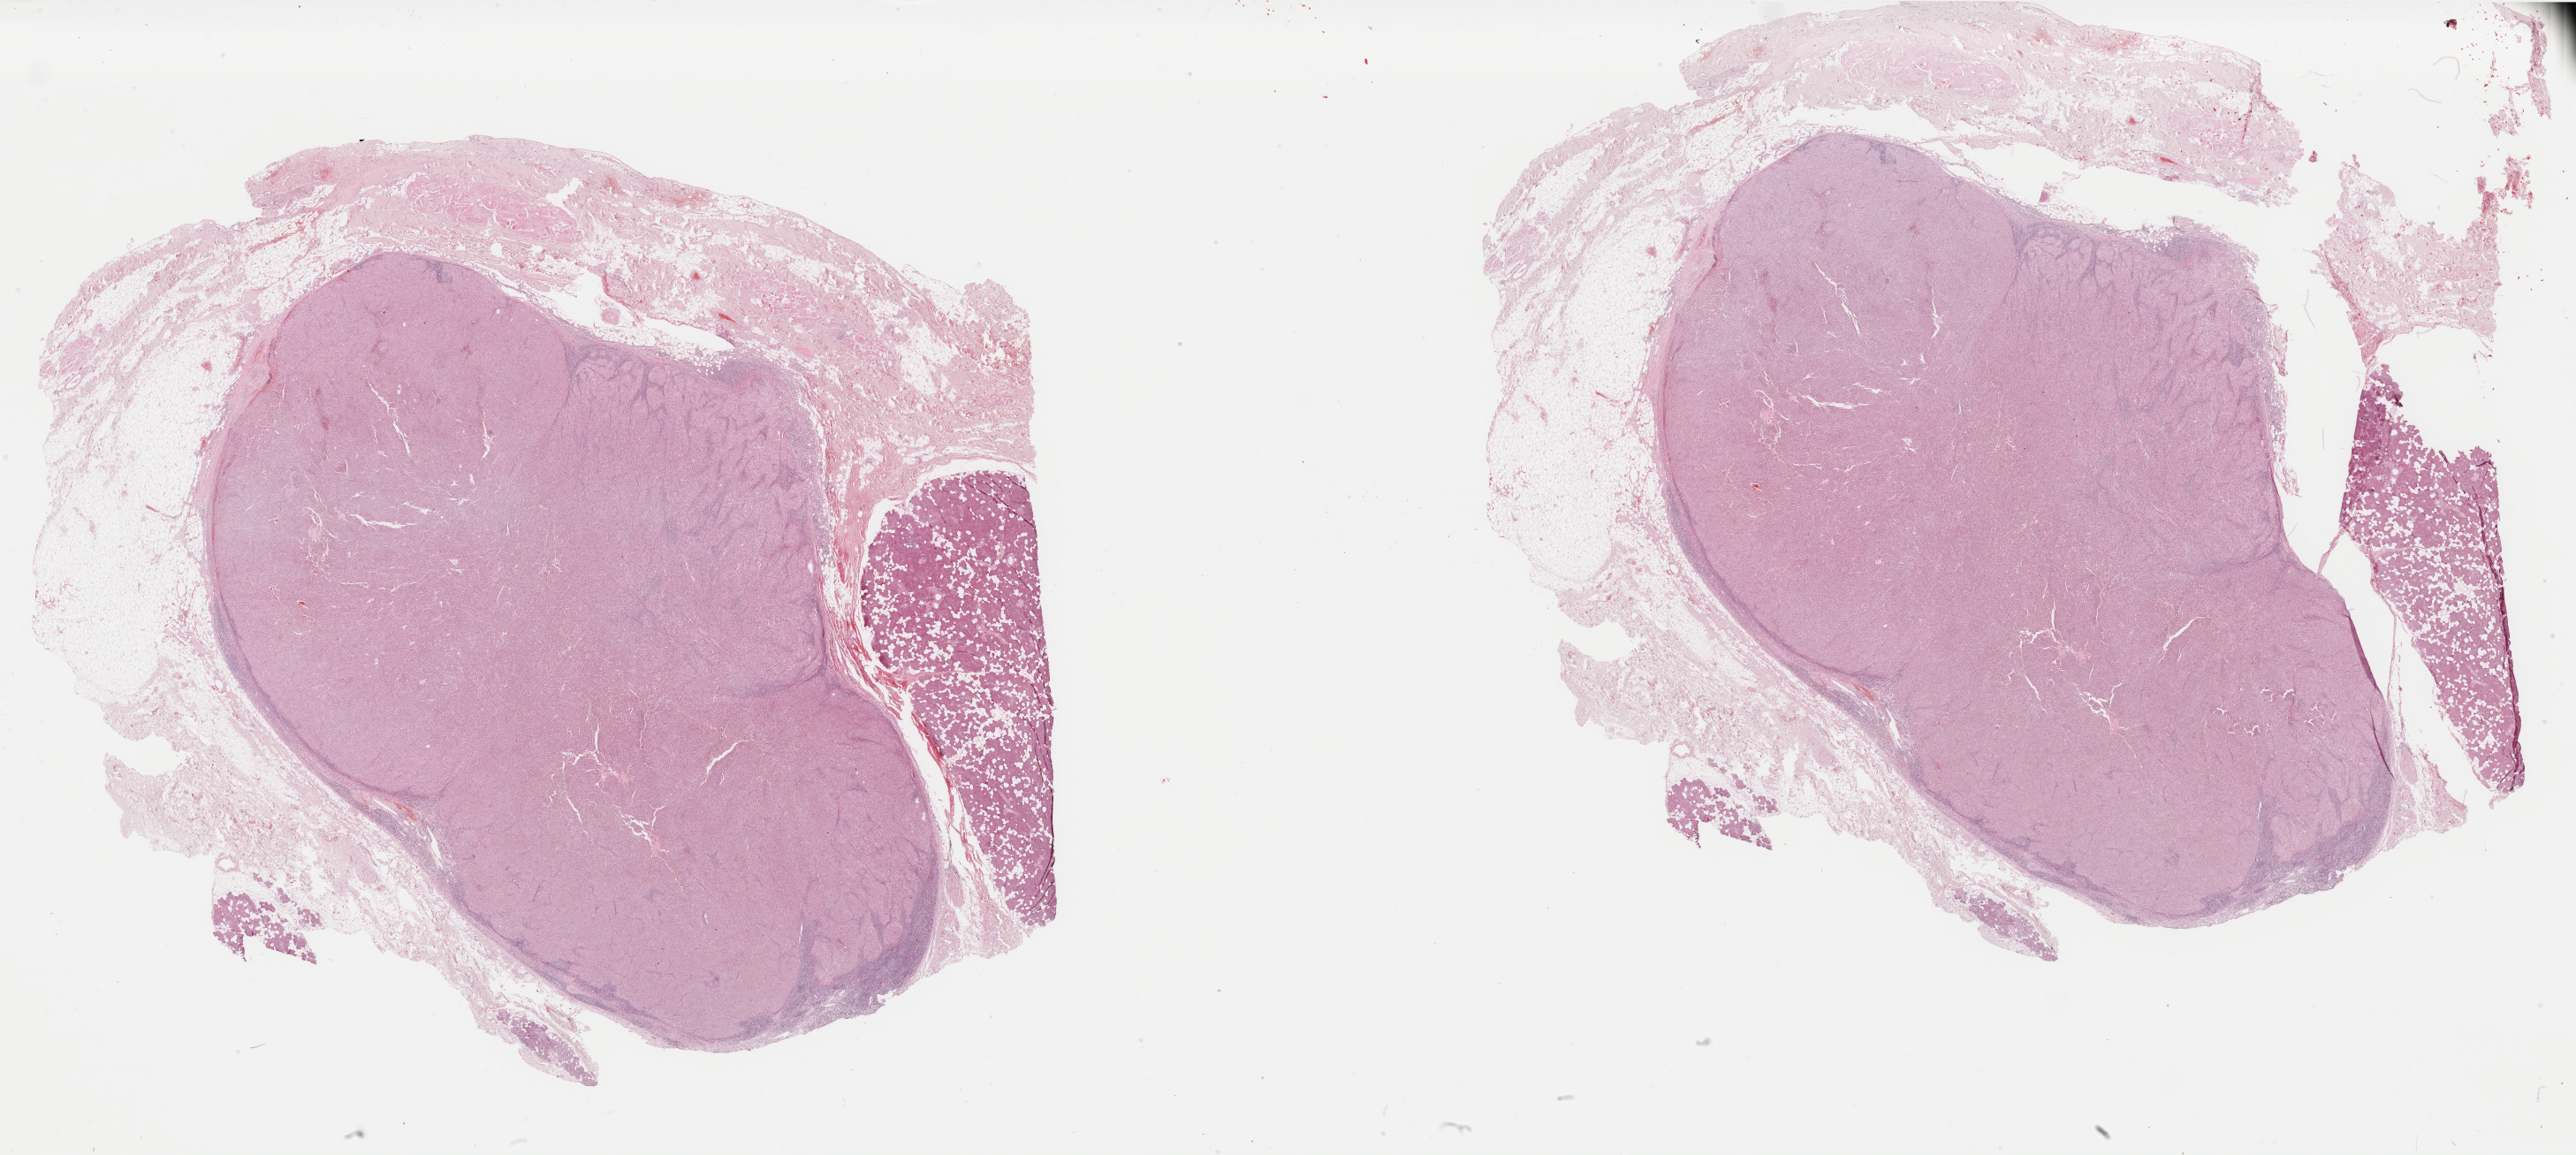
Whole-slide histology image, H&E-stained — shown as a low-resolution overview of the whole scanned area (about 46.3 x 20.7 mm, acquisition: 40x scan), formalin-fixed paraffin-embedded (FFPE) diagnostic section, metastatic tumour sample, sampled site not recorded. Patient: male, age at initial diagnosis 82 years.
* this section: metastatic tumour tissue
* patient diagnosis: Malignant melanoma, NOS